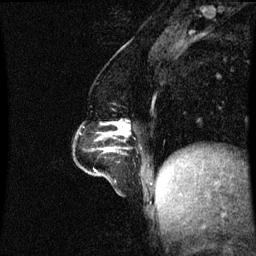
Breast MRI (dynamic contrast-enhanced), one sagittal slice; position 23 of 60 along the scan axis; dynamic contrast-enhanced series, image 2 of 3 at this slice position (ordered by acquisition); 1.5 T; TE 4.2 ms, TR 8.9 ms; 2.1 mm slice thickness; 256 × 256 image matrix, field of view 200 × 200 mm. Female patient, age 47 years. Case-level facts recorded for this patient, not image findings: setting: breast cancer imaged before/during neoadjuvant chemotherapy; receptor status: HR-positive, HER2-negative.
Structures marked on this image (semi-automatic segmentation, software-assisted and operator-edited):
- analysis volume of interest (the breast-tissue region the enhancement analysis was run in; not a lesion): bounding box <74,122,131,153> (left, top, right, bottom; pixels)
- tumour enhancement mask (voxels above the 70 % enhancement threshold inside the analysis volume of interest): <115,122,130,135>